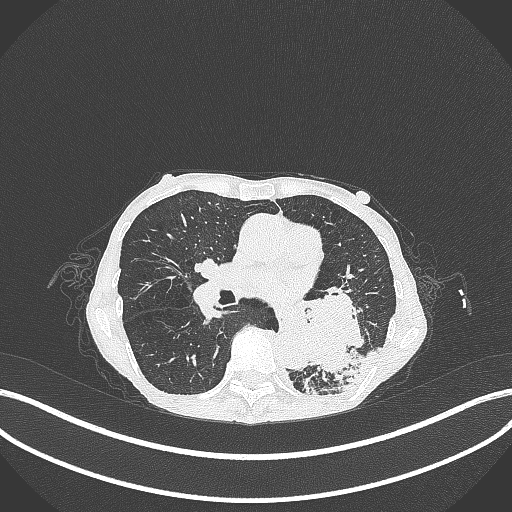
Chest CT, one axial slice; slice 139 of 347 in the series (ordered by position); reconstruction kernel B70f; lung window (W 1500 / L -600 HU); 1 mm slice thickness; 512 × 512 image matrix, field of view 400 × 400 mm. Patient: female, 70 years. Case-level facts recorded for this patient, not image findings: clinical TNM (as recorded): T3 N0 M0.
Annotated regions visible in this slice (bounding box drawn by a radiologist):
- lung tumour (recorded histology: small cell carcinoma): box from (x=297, y=281) to (x=366, y=380) px